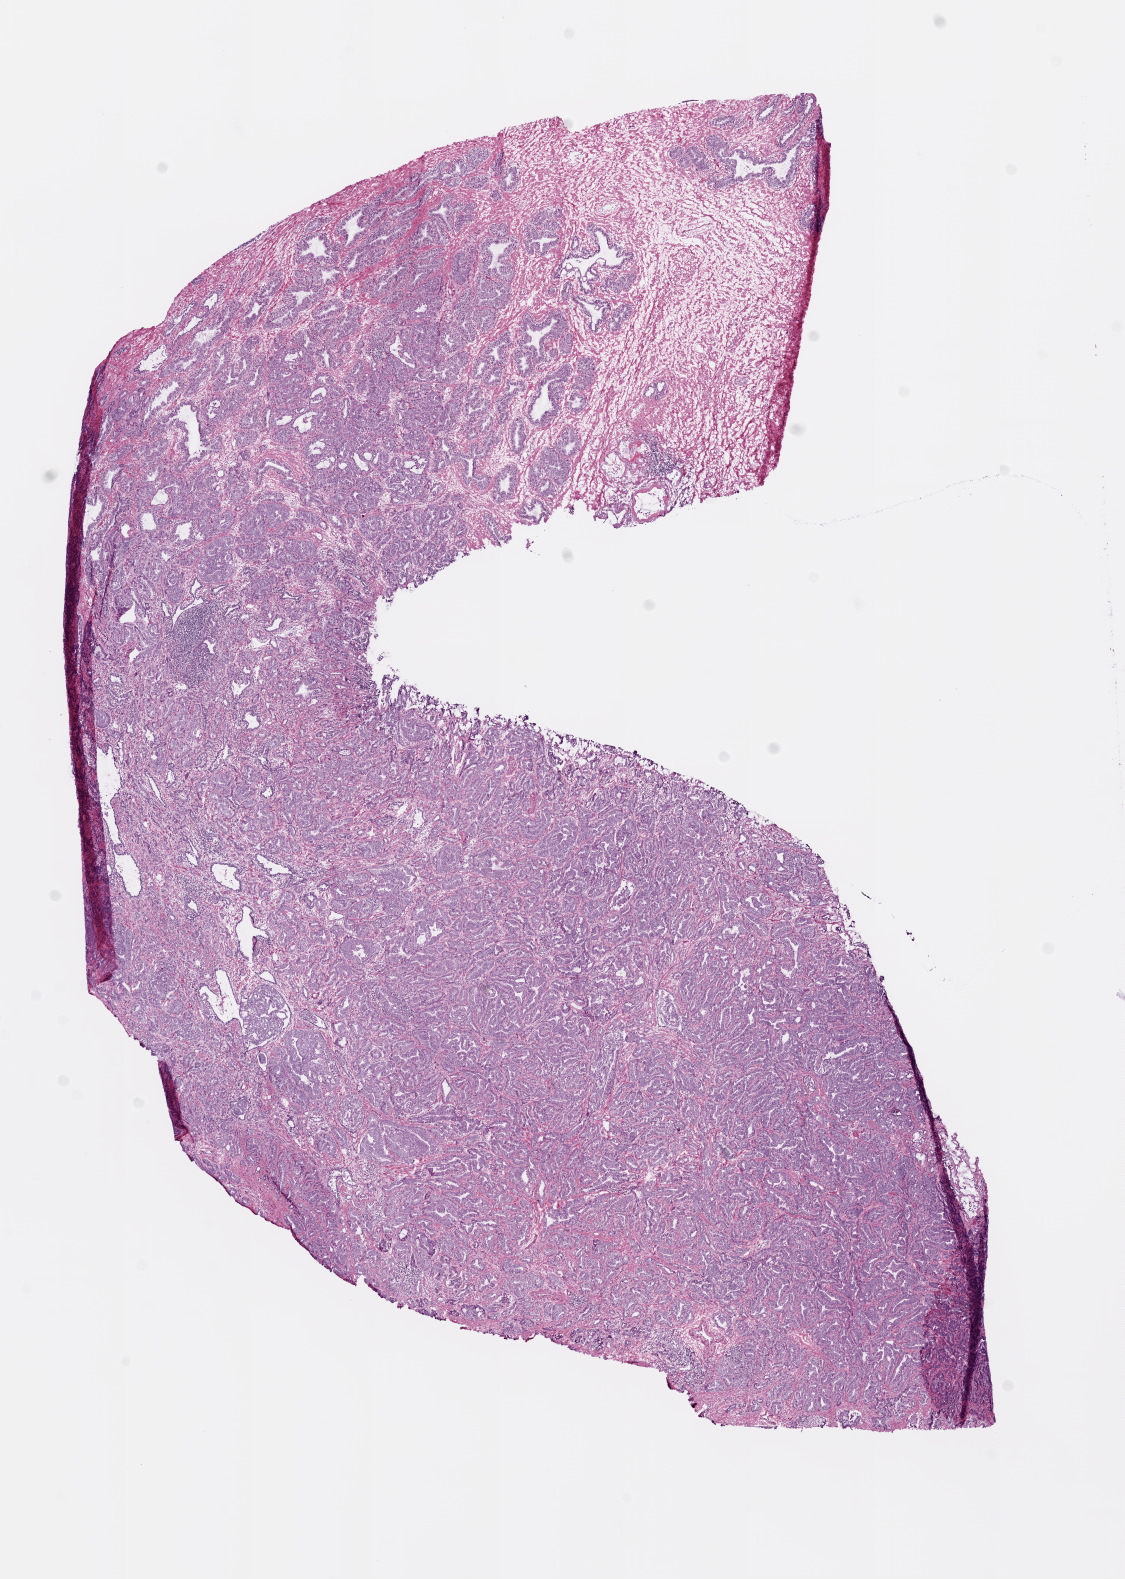
Digitized H&E-stained tissue section (whole slide) — low-resolution overview of the scanned area, about 9.0 x 12.7 mm (from a 20x scan), frozen section, primary tumour sample from the prostate. Male, age 57 years at initial diagnosis. Gleason score: 7 (3+4). Slide review estimates, as recorded: tumour cells 75%, tumour nuclei 80%, normal cells 12%, stromal cells 13%, necrosis 0%. Inflammatory infiltration, as recorded: lymphocyte infiltration 3%, monocyte infiltration 0%, neutrophil infiltration 0%.
- lymph nodes positive (case pathology): 0 of 4 examined
- histologic diagnosis: Acinar cell carcinoma (prostate gland)
- laterality: bilateral